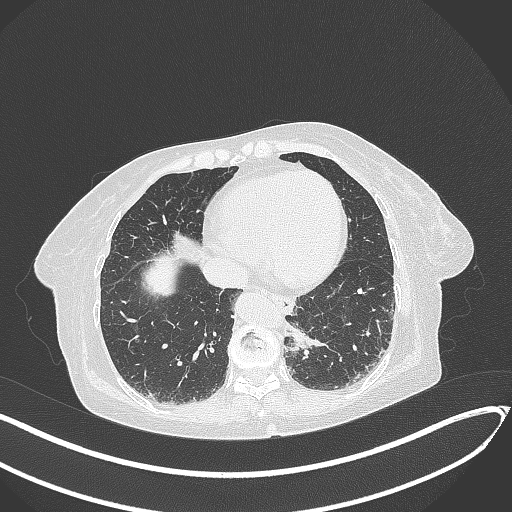
Chest CT, one axial slice; position 58 of 324 along the scan axis; 120 kVp; lung window (W 1500 / L -600 HU); 512 × 512 image matrix, field of view 400 × 400 mm. Female patient, age 82 years. From the clinical record (not read from this slice): clinical TNM (as recorded): T1b N0 M1.
Structures marked on this image (bounding box drawn by a radiologist):
- lung tumour (recorded histology: adenocarcinoma): bounding box (x1, y1, x2, y2) in pixels: (286, 321, 323, 360)